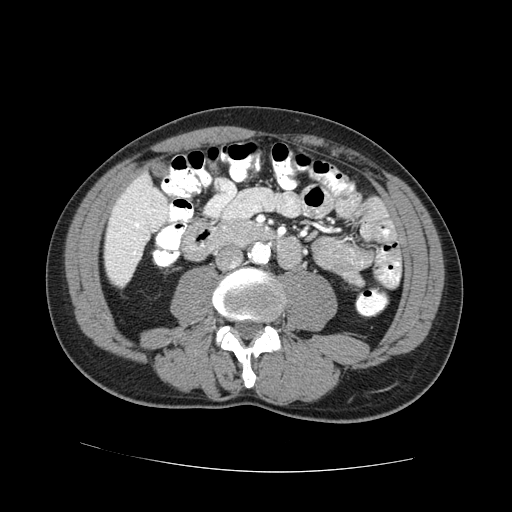
Contrast-enhanced abdominal CT (liver protocol), one axial slice; position 11 of 73 along the scan axis; reconstruction kernel STANDARD; one of 2 acquisitions stored at this slice position; soft-tissue window (W 400 / L 40 HU); 512 × 512 image matrix, field of view 380 × 380 mm. From the clinical record (not read from this slice): diagnosis: hepatocellular carcinoma (patient treated with transarterial chemoembolisation; whether this scan precedes or follows treatment is not stated here); TNM stage (as recorded): Stage-IVA; Child-Pugh class: A; tumour differentiation: no biopsy; tumour nodularity: uninodular.
Outlined on this slice (semi-automatic segmentation, software-assisted and operator-edited):
- liver parenchyma outside the tumour (the mass and vessels are separate outlines, so this box may not span the whole liver): bounding box (x1, y1, x2, y2) in pixels: (104, 172, 168, 286)
- liver vessels: (127, 210, 155, 254)